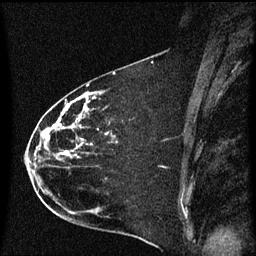
Breast MRI (dynamic contrast-enhanced), one sagittal slice; position 34 of 60 along the scan axis; dynamic contrast-enhanced series, image 2 of 3 at this slice position (ordered by acquisition); 1.5 T; TE 4.2 ms, TR 8.4 ms; 2 mm slice thickness; 256 × 256 image matrix, field of view 200 × 200 mm. Female patient, age 35 years. Case-level facts recorded for this patient, not image findings: setting: breast cancer imaged before/during neoadjuvant chemotherapy; receptor status: HER2-positive.
Annotated regions visible in this slice (semi-automatically segmented with operator editing):
- analysis volume of interest (the breast-tissue region the enhancement analysis was run in; not a lesion): bounding box [x1, y1, x2, y2] px = [26, 68, 174, 173]
- tumour enhancement mask (voxels above the 70 % enhancement threshold inside the analysis volume of interest): [33, 92, 90, 173]